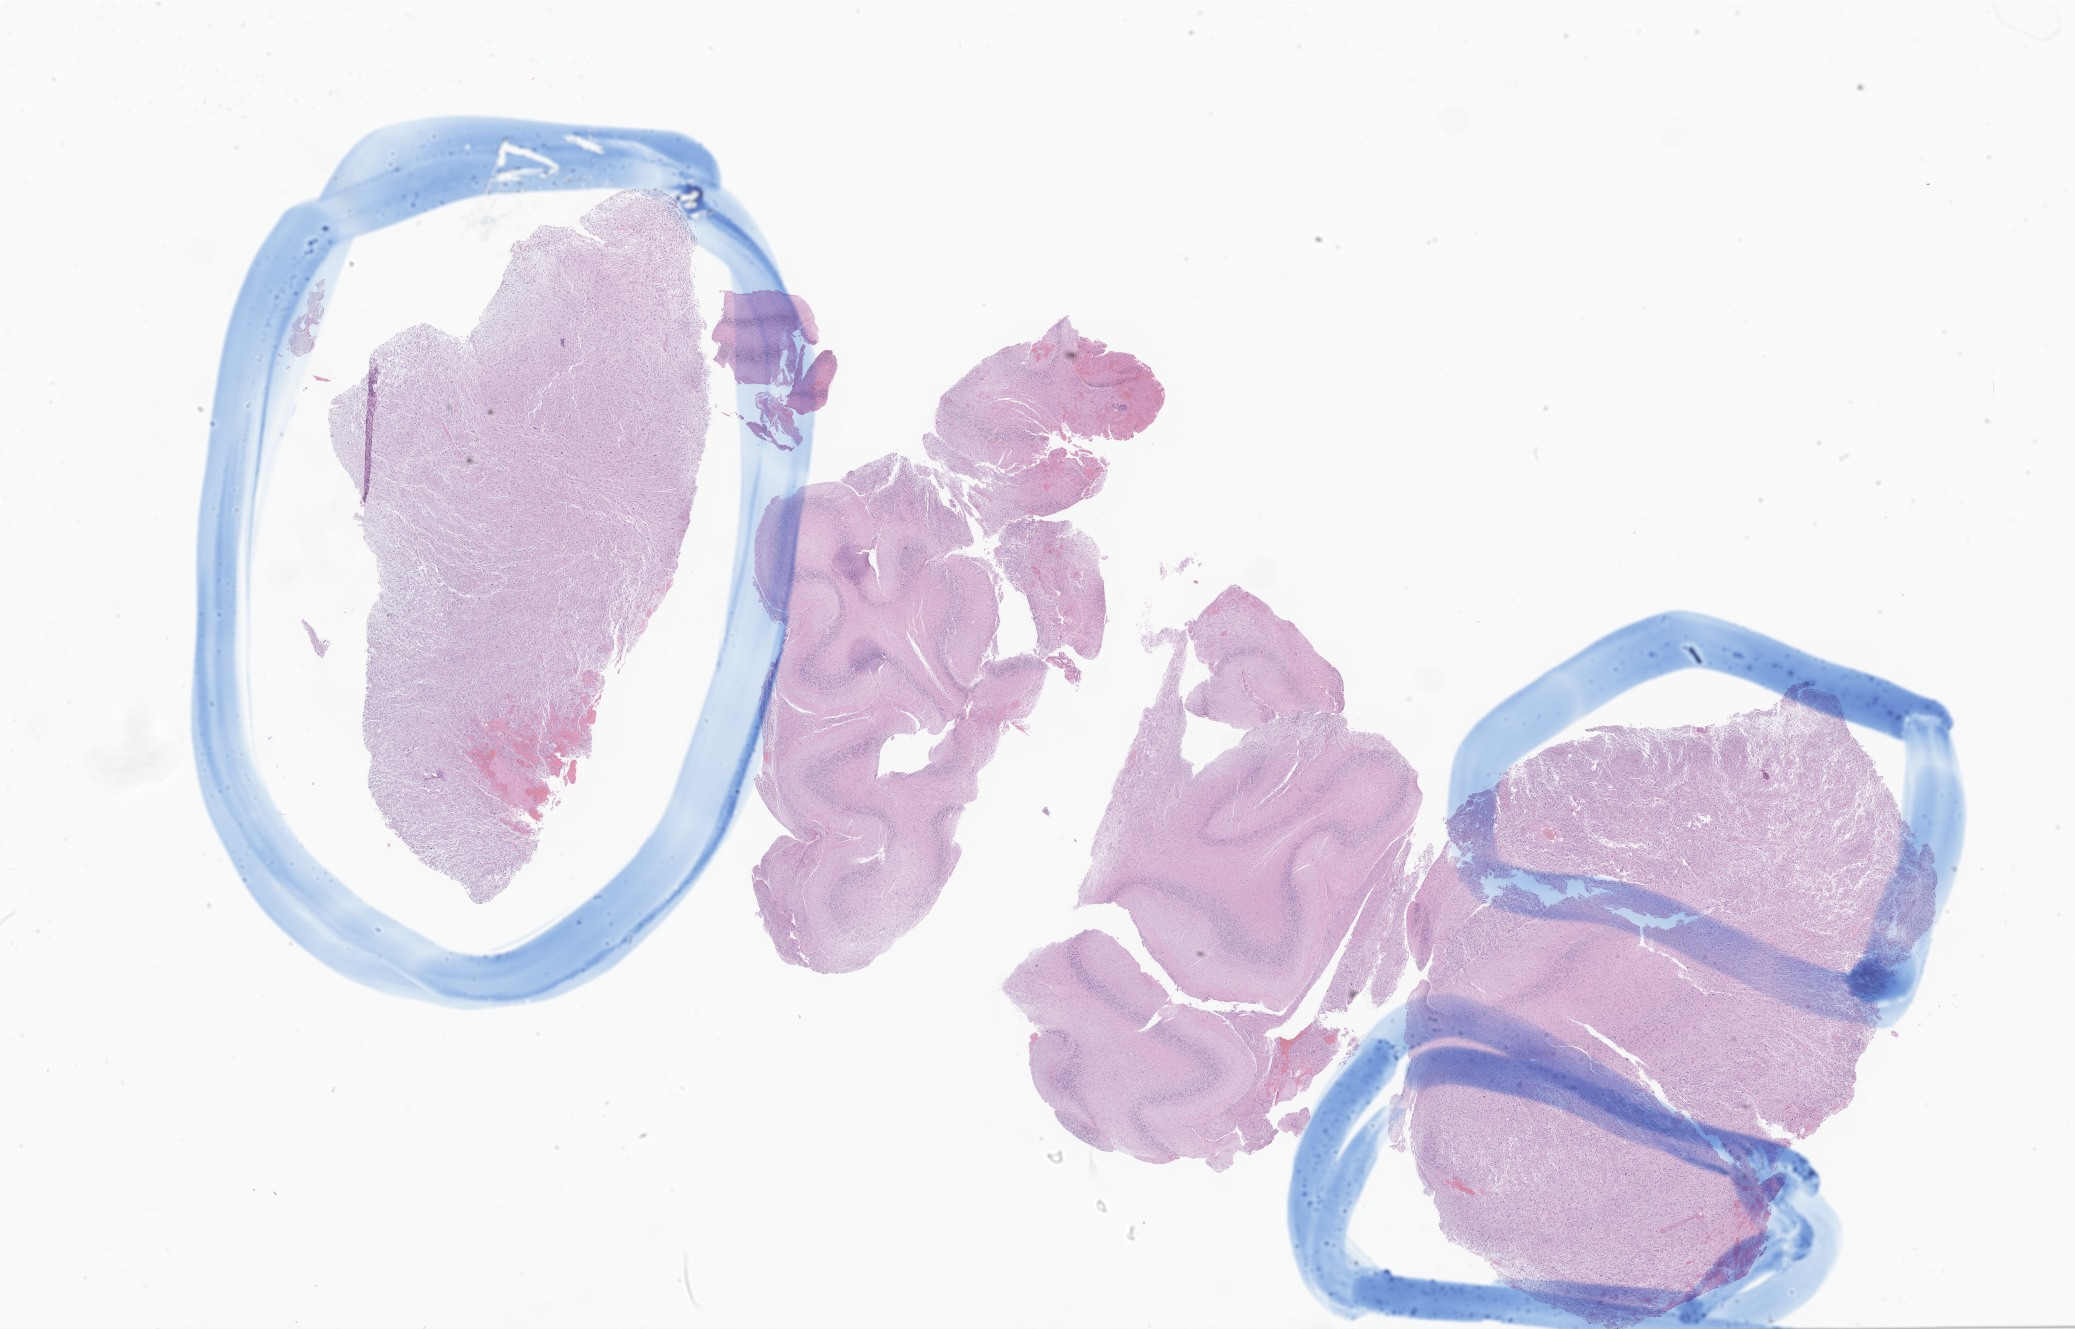
Whole-slide image, haematoxylin and eosin stain of tumor tissue from the cerebellum — low-resolution overview of the scanned area, about 35.0 x 22.4 mm. FFPE section. Patient: female, age 246 months.
Diagnosis: Astrocytoma, NOS.